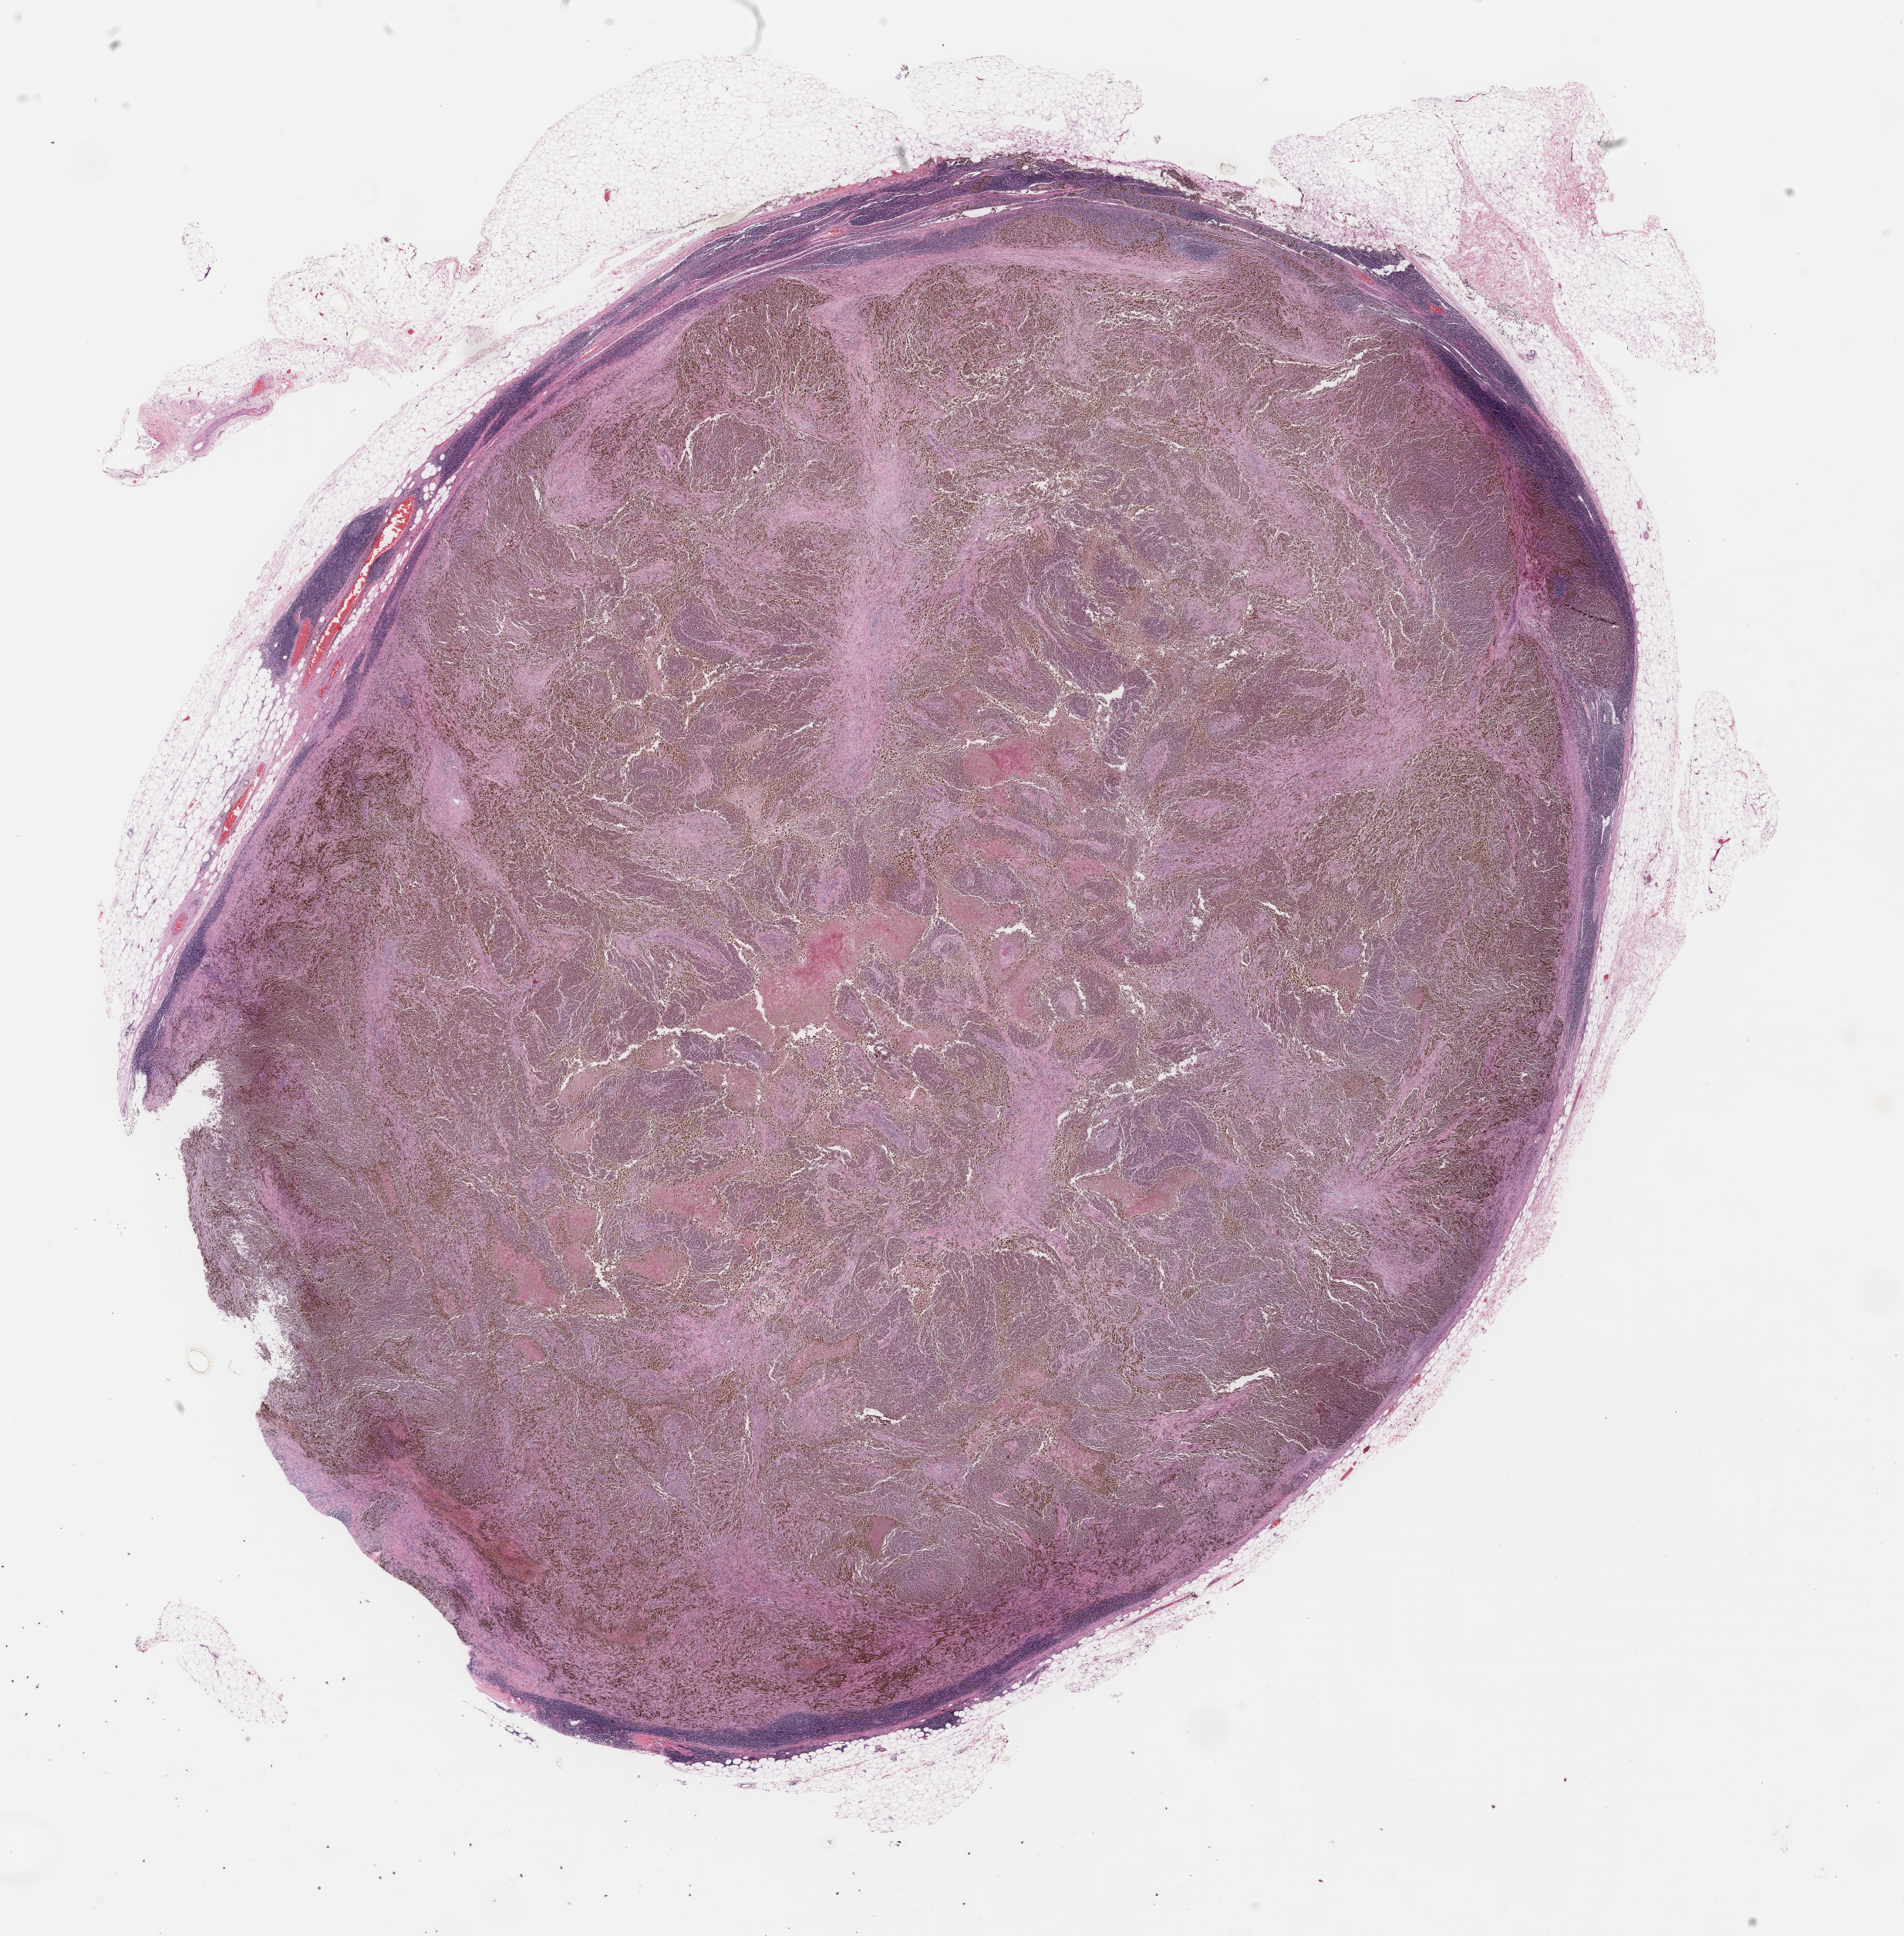
Hematoxylin and eosin (H&E) stained whole-slide image, low-resolution overview of the scanned area, about 19.6 x 19.9 mm. FFPE section. Sample: primary tumour, skin. Patient: male, age at initial diagnosis 56 years.
Histologic diagnosis: Malignant melanoma, NOS.